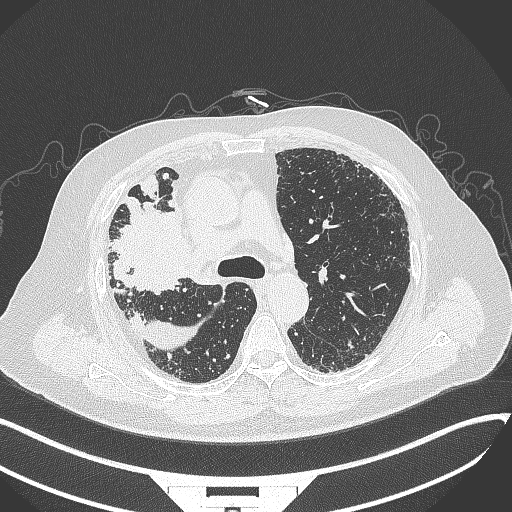
Chest CT, one axial slice. Slice 231 of 384 in the series (ordered by position). Reconstruction kernel B70f. 120 kVp. Lung window (W 1500 / L -600 HU). 1 mm slice thickness. 512 × 512 image matrix, field of view 400 × 400 mm. Male patient, age 69 years. From the clinical record (not read from this slice): clinical TNM (as recorded): T4 N3 M1.
Outlined on this slice (bounding box drawn by a radiologist):
- lung tumour (recorded histology: adenocarcinoma): bounding box [x1, y1, x2, y2] px = [112, 196, 192, 291]